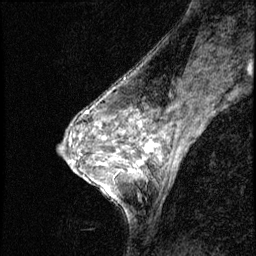
Breast MRI (dynamic contrast-enhanced), one sagittal slice. Position 32 of 56 along the scan axis. Dynamic contrast-enhanced series, image 2 of 3 at this slice position (ordered by acquisition). 1.5 T. TE 4.2 ms, TR 8.7 ms. 2.5 mm slice thickness. 256 × 256 image matrix, field of view 180 × 180 mm. Female patient, age 50 years. From the clinical record (not read from this slice): setting: breast cancer imaged before/during neoadjuvant chemotherapy; receptor status: HR-positive, HER2-negative.
Outlined on this slice (semi-automatic segmentation, software-assisted and operator-edited):
- analysis volume of interest (the breast-tissue region the enhancement analysis was run in; not a lesion): bounding box <119,136,169,190> (left, top, right, bottom; pixels)
- tumour enhancement mask (voxels above the 140 % enhancement threshold inside the analysis volume of interest): <130,144,153,171>